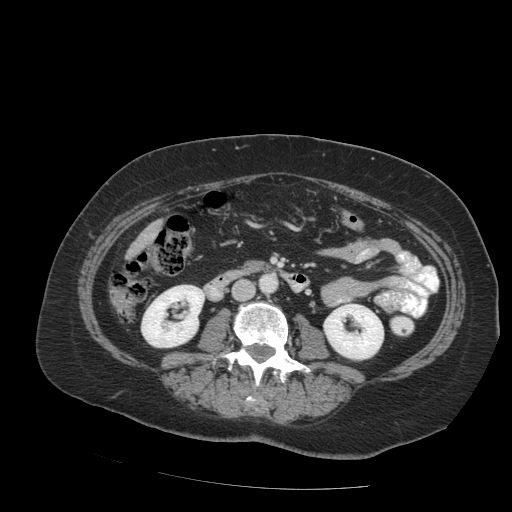
Contrast-enhanced abdominal CT (liver protocol), one axial slice; position 19 of 99 along the scan axis; reconstruction kernel STANDARD; 140 kVp; soft-tissue window (W 400 / L 40 HU); 2.5 mm slice thickness; 512 × 512 image matrix. Case-level facts recorded for this patient, not image findings: diagnosis: hepatocellular carcinoma (patient treated with transarterial chemoembolisation; whether this scan precedes or follows treatment is not stated here); TNM stage (as recorded): Stage-IVB; Child-Pugh class: A; tumour differentiation: moderately differentiated; tumour nodularity: uninodular.
Structures marked on this image (semi-automatic segmentation, software-assisted and operator-edited):
- liver parenchyma outside the tumour (the mass and vessels are separate outlines, so this box may not span the whole liver): bounding box <128,220,161,256> (left, top, right, bottom; pixels)